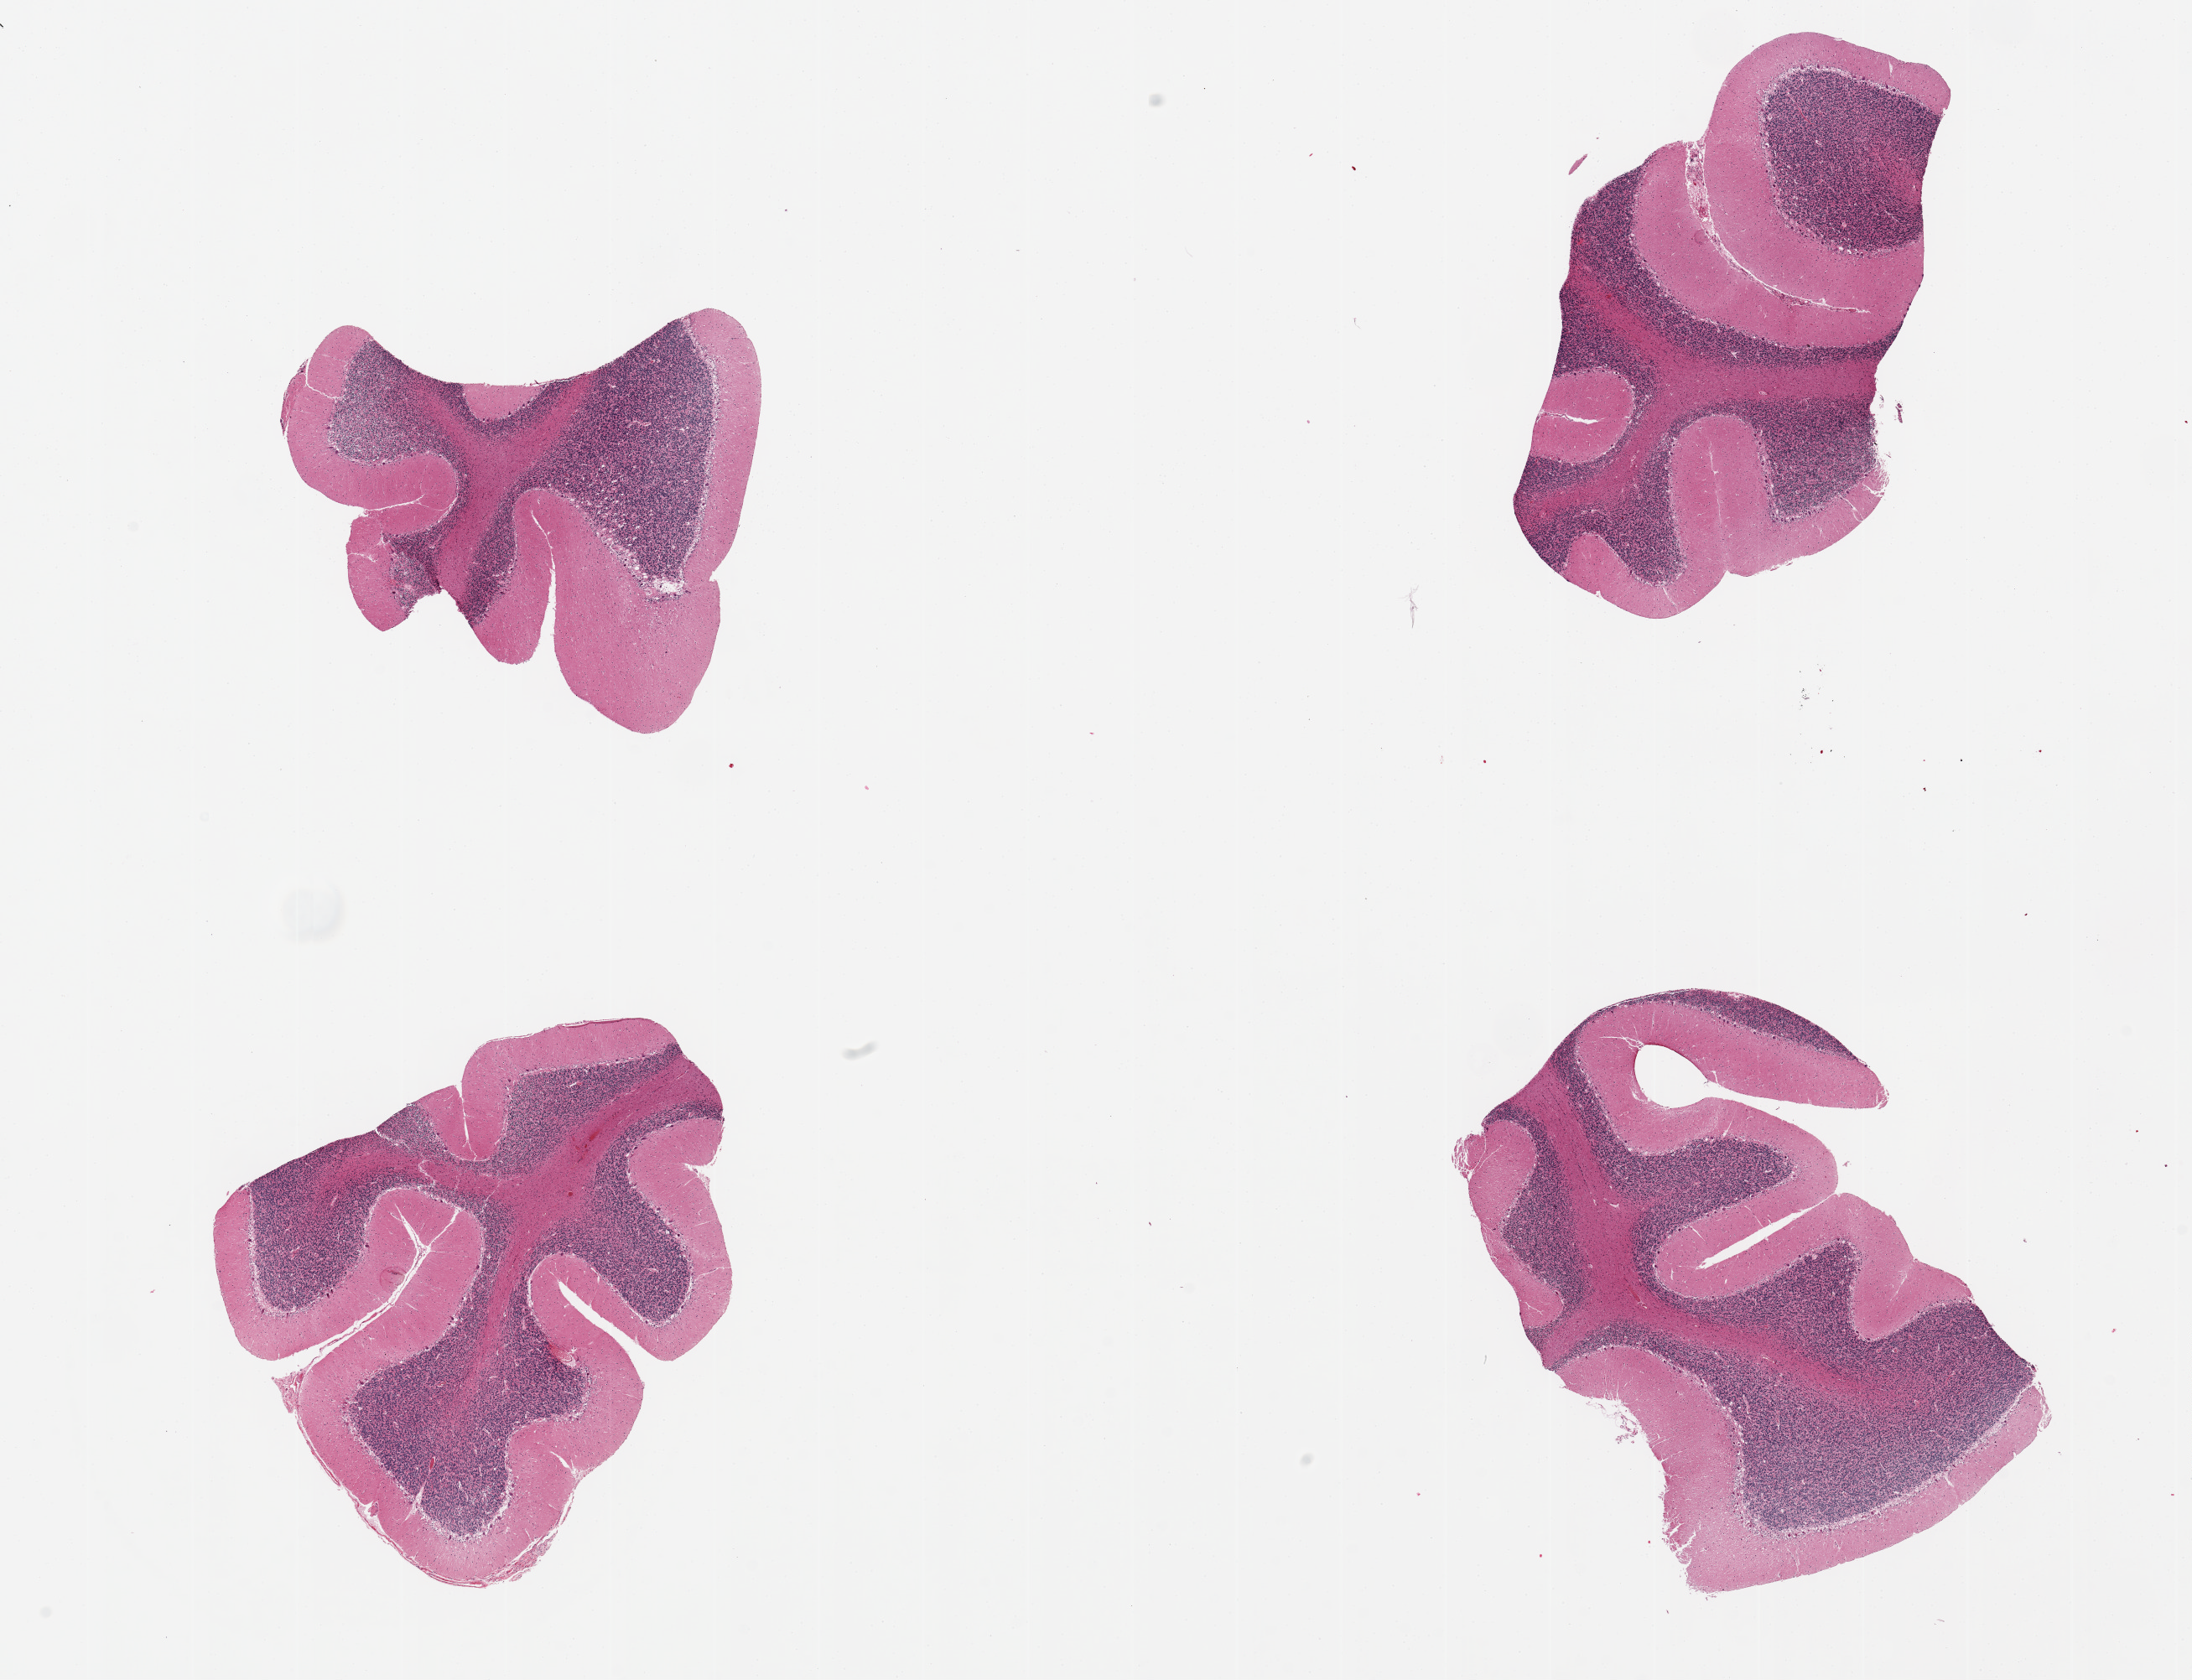
Whole-slide image, H&E stain, whole scanned area (about 20.7 x 15.8 mm) shown as a low-resolution overview, PAXgene-fixed paraffin-embedded (PFPE) section, sampled site (target tissue): cerebellum, tissue donor sample. Male donor.
Pathologist's review note for this sample: 4 pieces. up to 6x4mm; Purkinje cells well visualized, minimal ischemic changes.